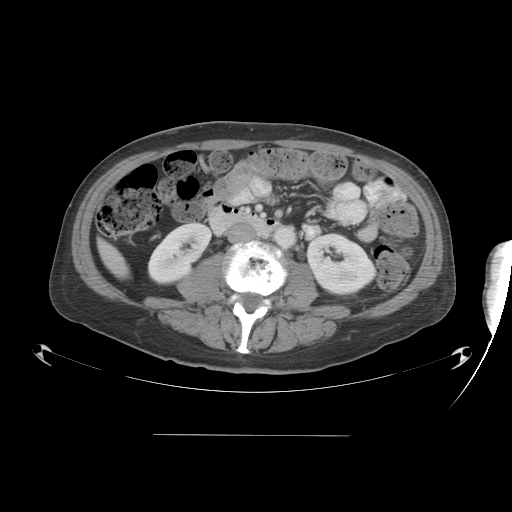
Contrast-enhanced abdominal CT, one axial slice. Position 9 of 48 along the scan axis. Reconstruction kernel STANDARD. 120 kVp. Soft-tissue window (W 400 / L 40 HU). 5 mm slice thickness. 512 × 512 image matrix, field of view 486 × 486 mm. Male patient, age 65 years. Case-level facts recorded for this patient, not image findings: diagnosis: colorectal cancer liver metastases, imaged before liver resection; multiple liver metastases: yes.
Structures marked on this image (manually delineated by an expert):
- liver: bounding box [x1, y1, x2, y2] px = [101, 244, 126, 275]